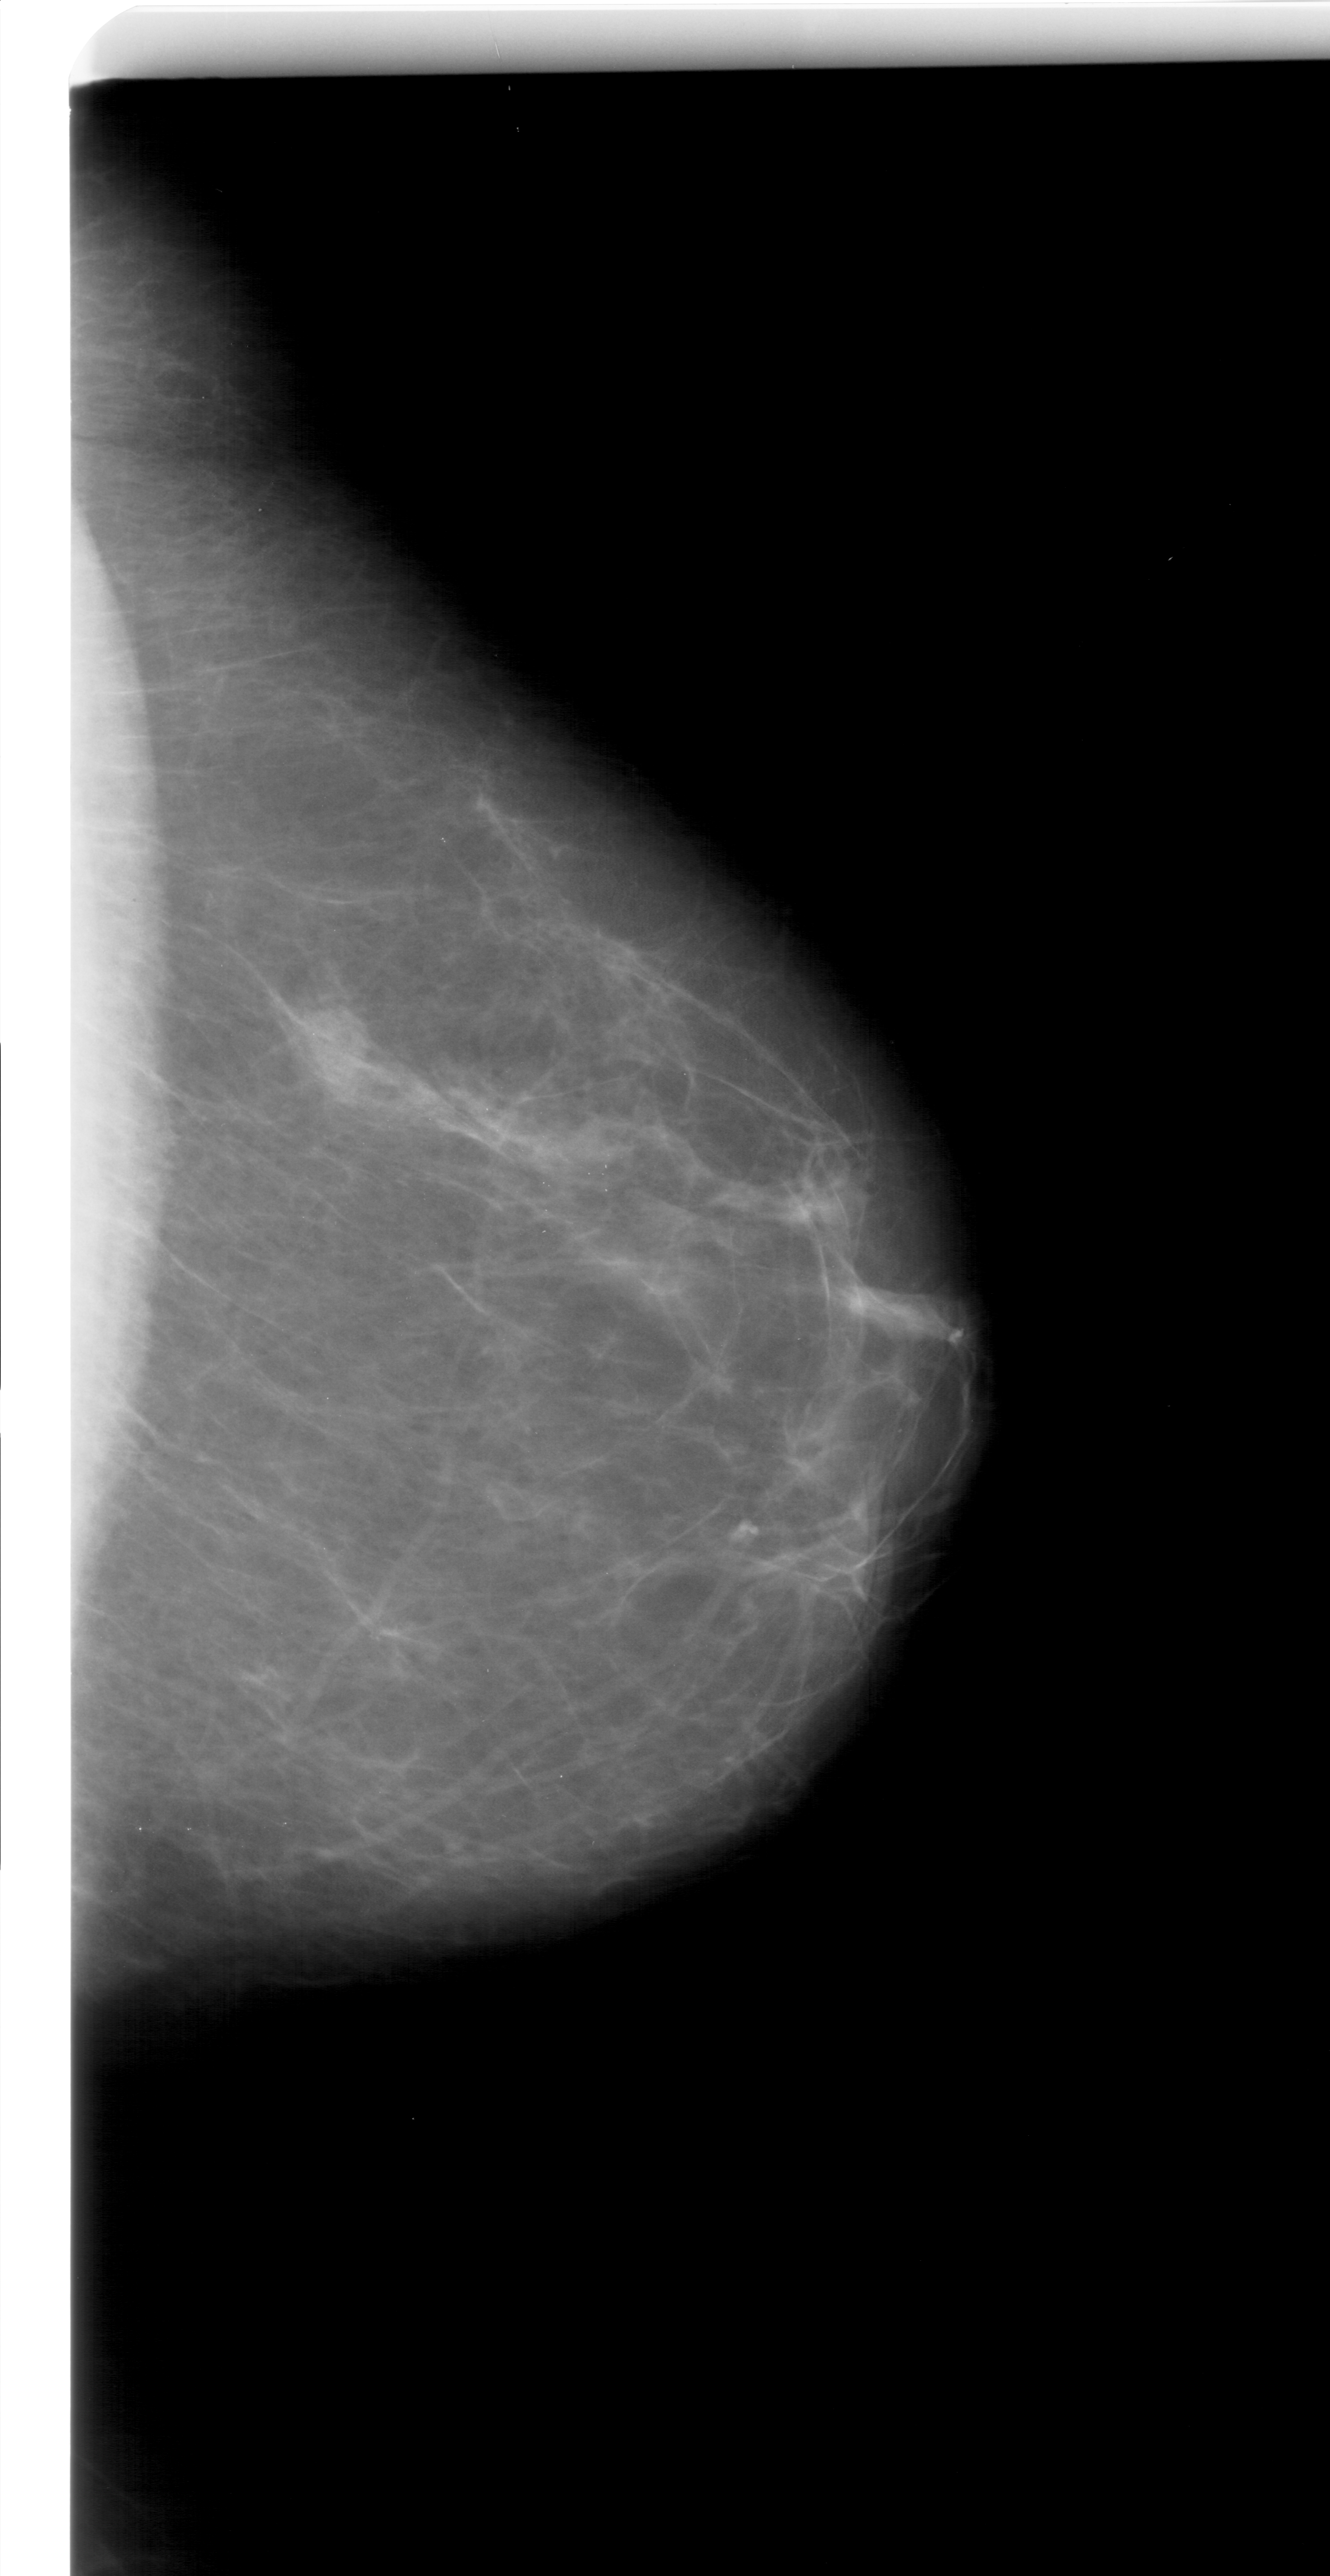
Digitized screen-film mammogram, right breast, craniocaudal (CC) view, BI-RADS breast density category 2 (scale 1–4).
- Abnormality record for this image: mass, shape focal asymmetric density, margins ill defined; BI-RADS assessment category 4; pathology result (as recorded, not read from the image): benign.